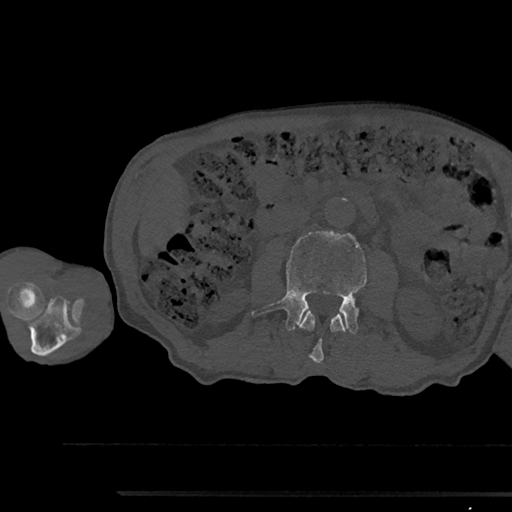
CT including the spine, one axial slice; slice 517 of 797 in the series (ordered by position); reconstruction kernel Br40s/3; 120 kVp; bone window (W 1800 / L 400 HU); 0.5 mm slice thickness; 512 × 512 image matrix. Male patient, age 79 years. From the clinical record (not read from this slice): primary cancer: prostate.
Outlined on this slice (semi-automatic segmentation, software-assisted and operator-edited):
- L2 vertebra: bounding box (x1, y1, x2, y2) in pixels: (299, 310, 347, 364)
- L3 vertebra: (252, 231, 366, 334)